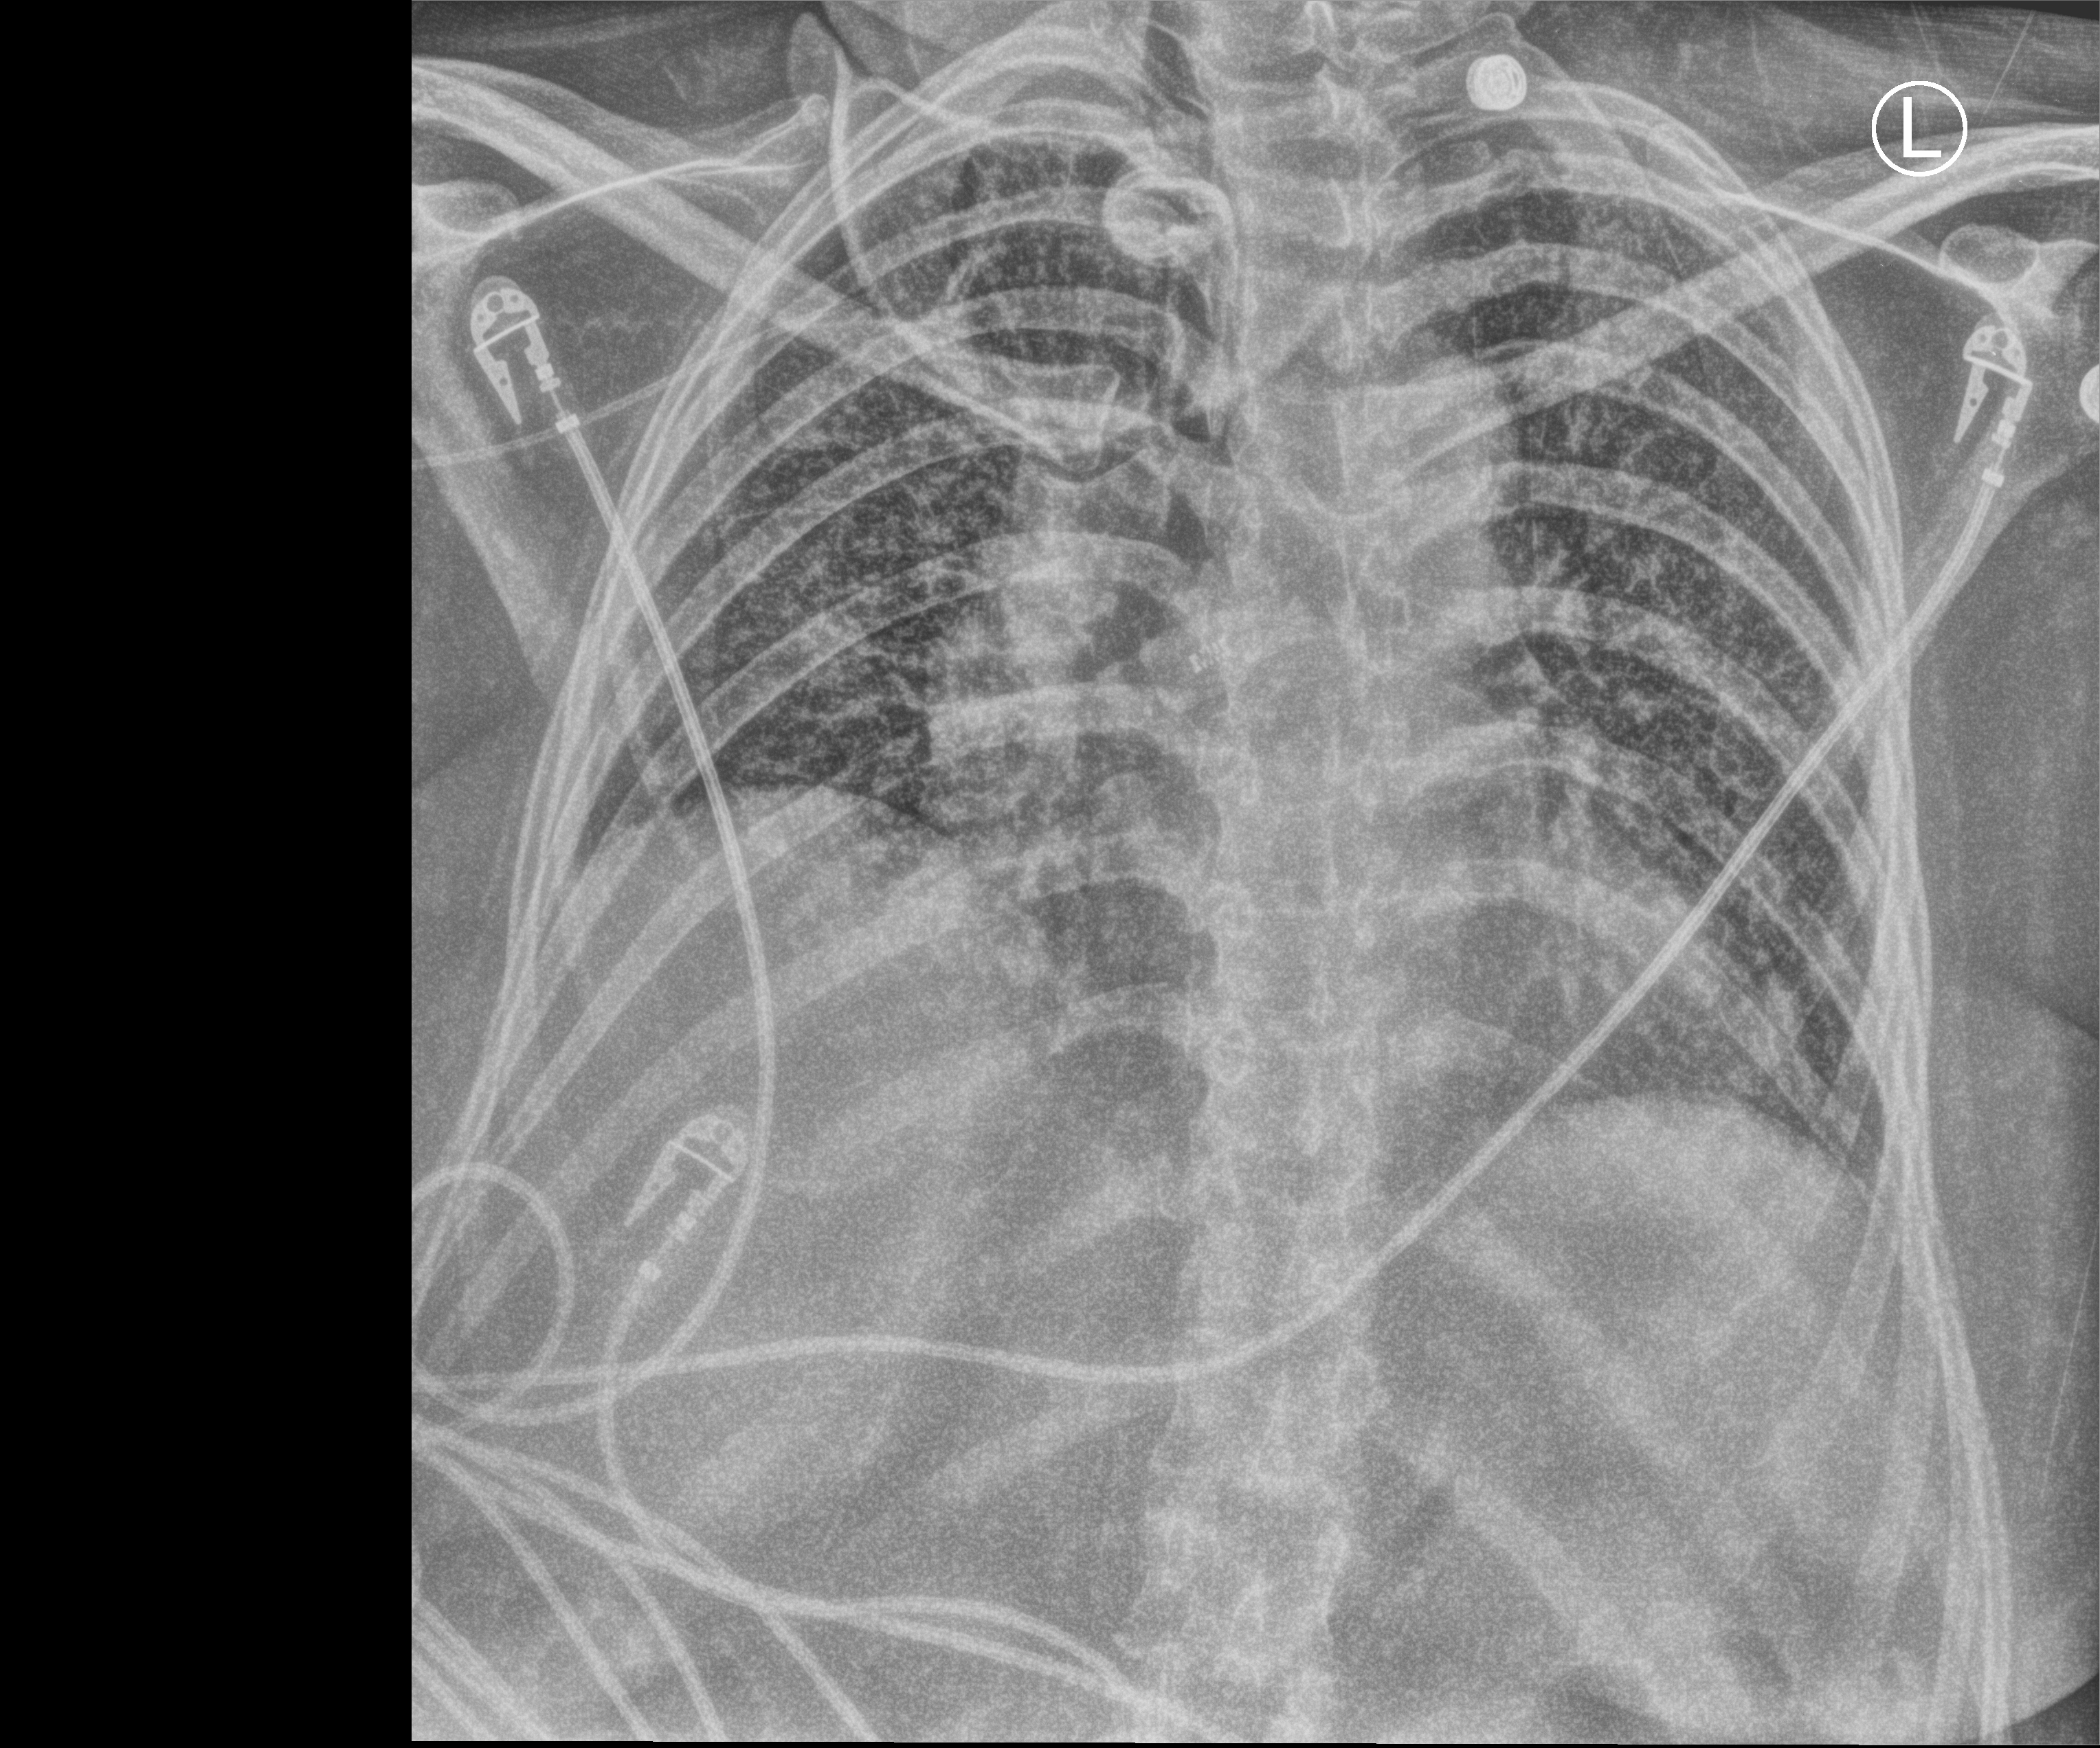
Bedside chest radiograph (computed radiography), anteroposterior (AP) projection. Patient hospitalised with COVID-19; female, aged 18–59 years.
Hospital-stay facts (about this admission, not read from this image; timing relative to this image not recorded):
- admitted to intensive care during this hospital stay: yes
- mechanically ventilated during this hospital stay: yes